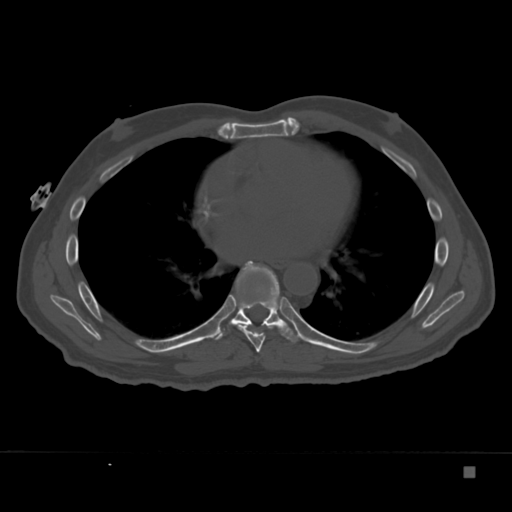
CT including the spine, one axial slice; slice 215 of 332 in the series (ordered by position); 120 kVp; bone window (W 1800 / L 400 HU); 1.5 mm slice thickness; 512 × 512 image matrix, field of view 389 × 389 mm. Male patient, age 72 years. Case-level facts recorded for this patient, not image findings: primary cancer: skeletal.
Structures marked on this image (semi-automatically segmented with operator editing):
- T7 vertebra: box from (x=237, y=324) to (x=274, y=353) px
- T8 vertebra: (x=212, y=260)–(x=305, y=342)